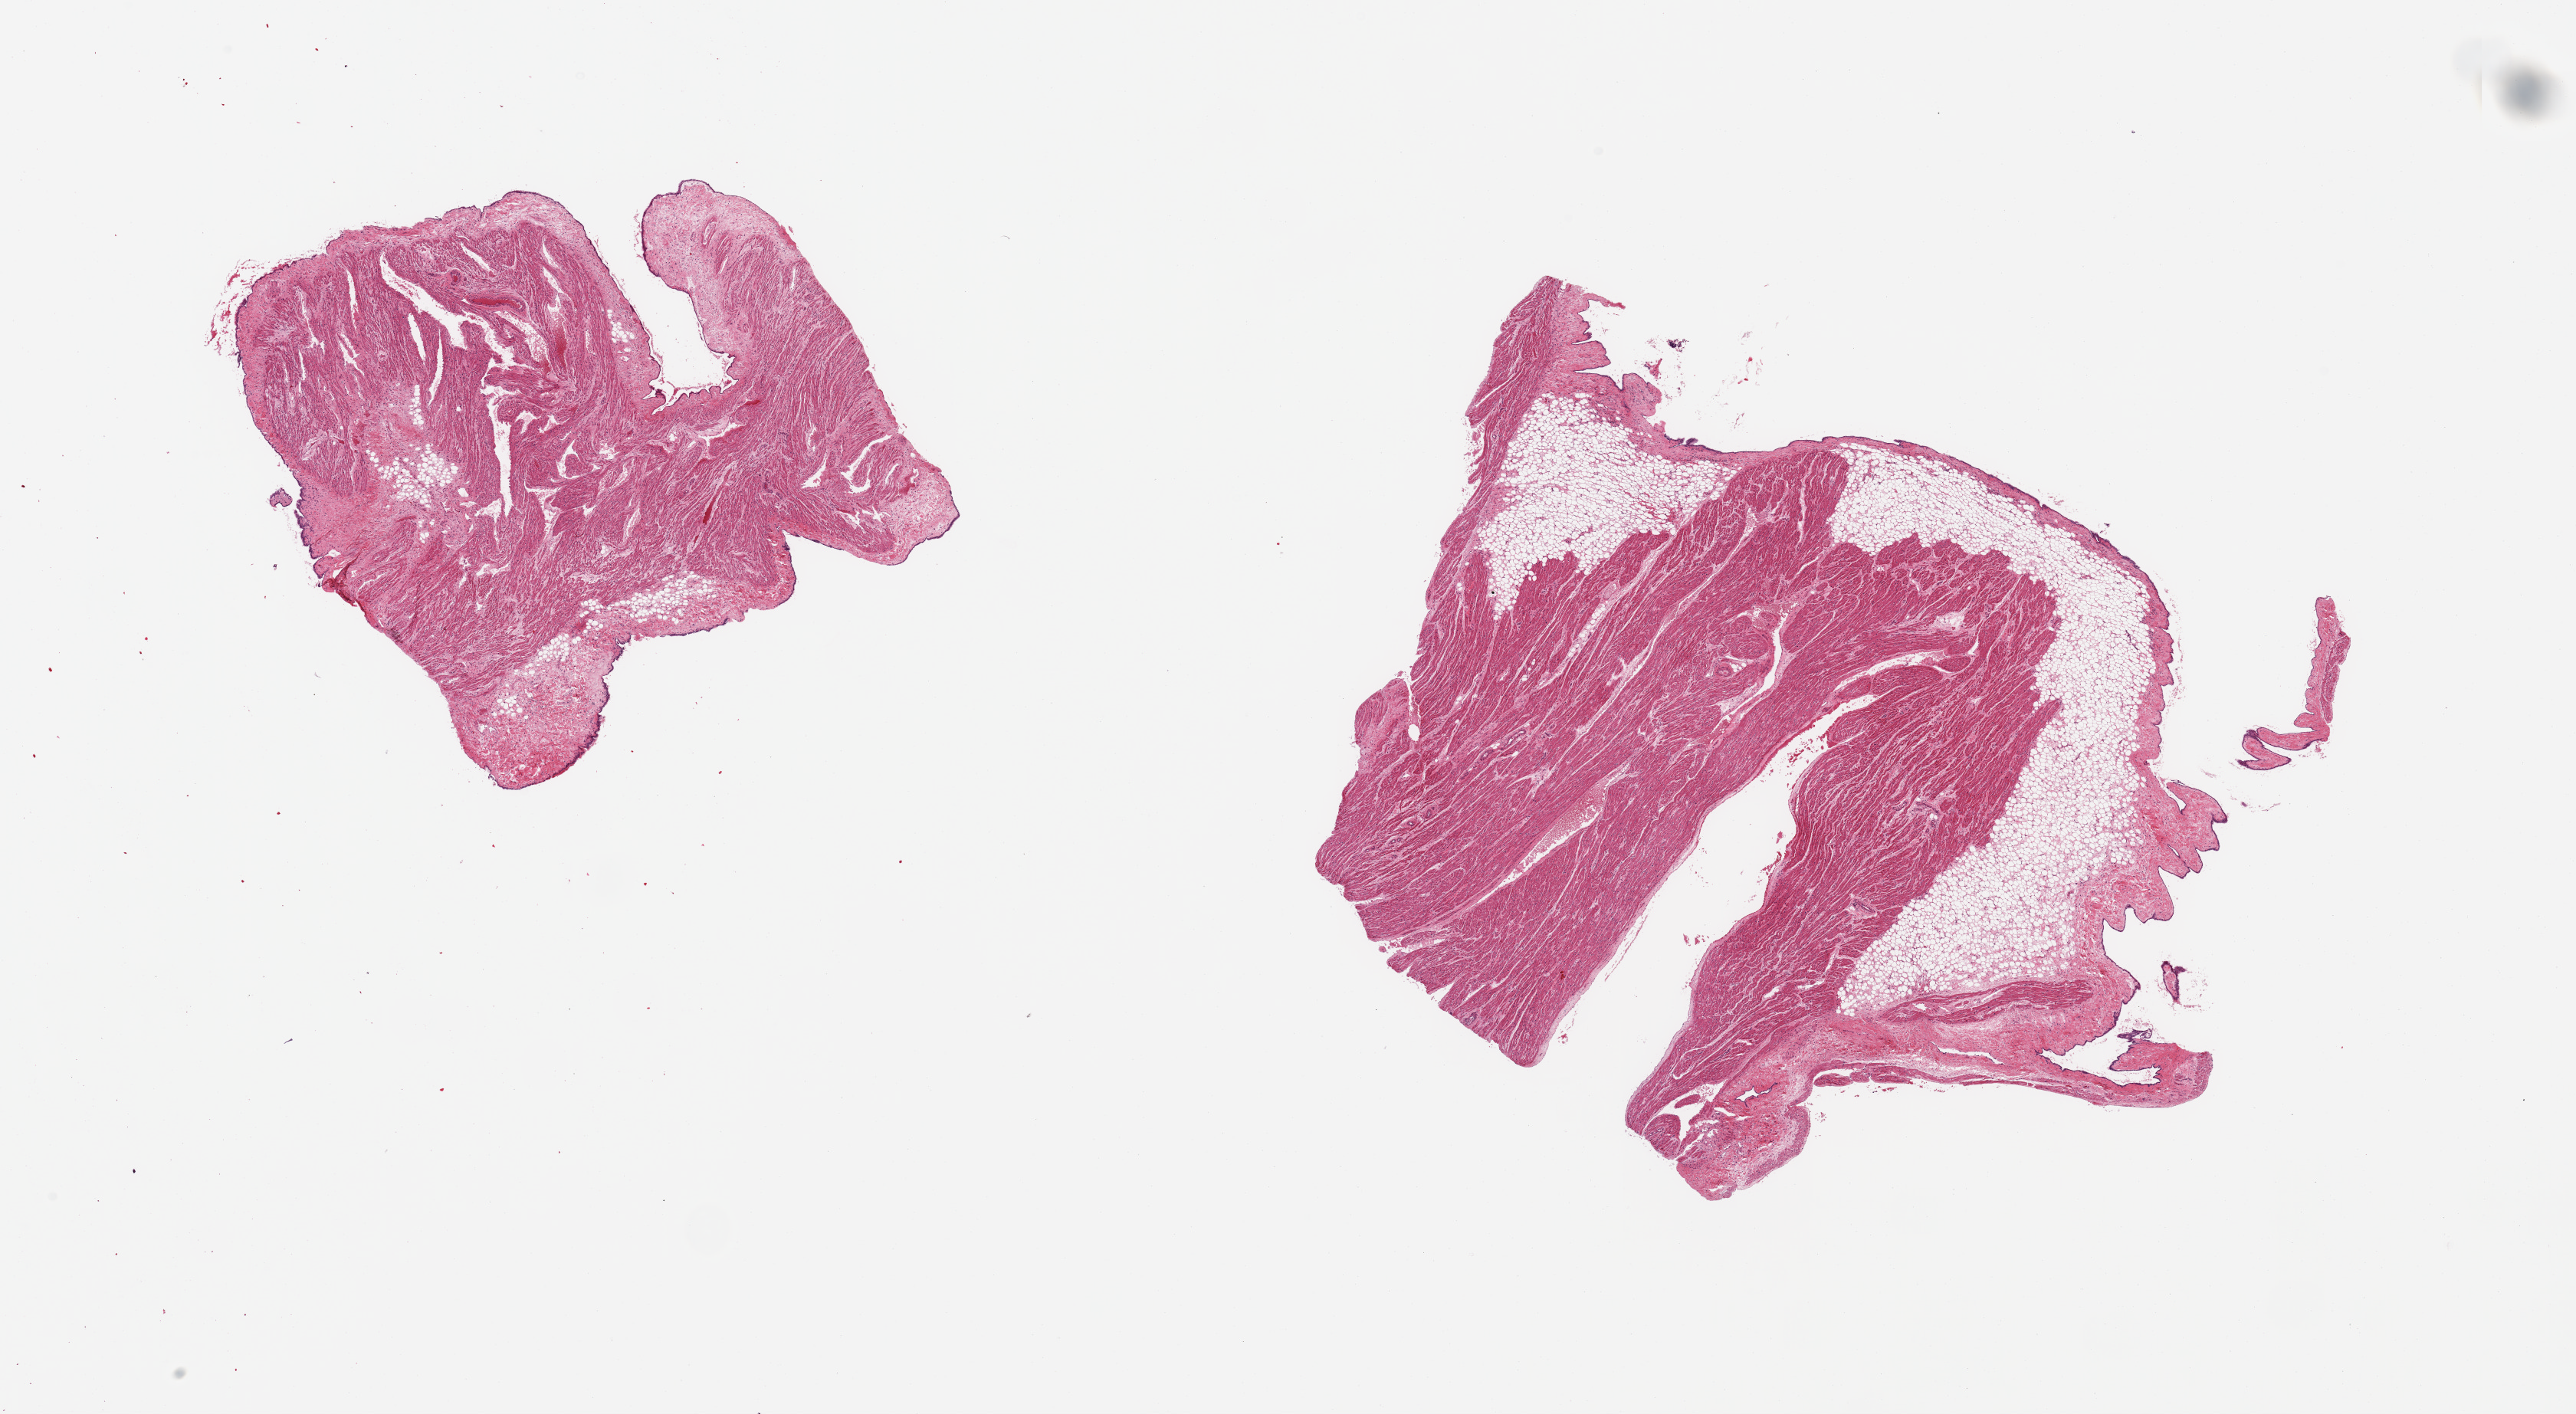
Haematoxylin and eosin whole-slide image — a low-resolution overview of the entire scanned area, about 26.6 x 14.6 mm, PAXgene-fixed paraffin-embedded (PFPE) section, sampled site (target tissue): auricular appendage, tissue donor sample. Male donor.
• reviewer comment on this tissue sample: 2 pieces, no abnormalities